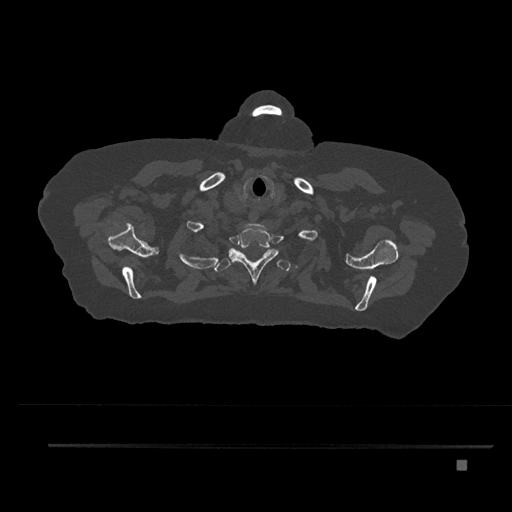
CT including the spine, one axial slice. Position 691 of 797 along the scan axis. Reconstruction kernel Br40s/3. 120 kVp. Bone window (W 1800 / L 400 HU). 512 × 512 image matrix, field of view 437 × 437 mm. Female patient, age 76 years. Case-level facts recorded for this patient, not image findings: primary cancer: lung.
Structures marked on this image (semi-automatically segmented with operator editing):
- T1 vertebra: bounding box <229,225,279,284> (left, top, right, bottom; pixels)
- T2 vertebra: <207,248,291,272>